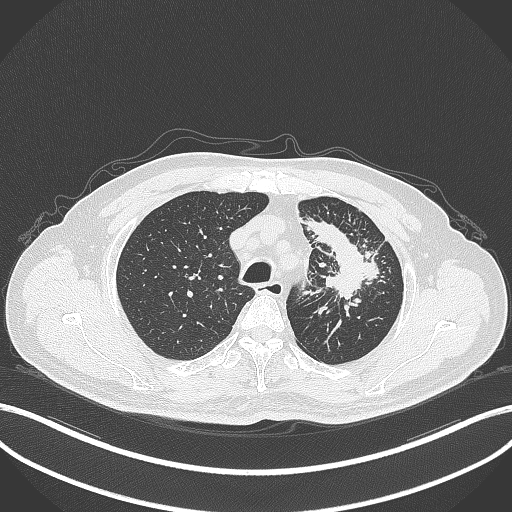
Chest CT, one axial slice; slice 279 of 386 in the series (ordered by position); reconstruction kernel B70f; 120 kVp; lung window (W 1500 / L -600 HU); 1 mm slice thickness; 512 × 512 image matrix, field of view 400 × 400 mm. Patient: male, 69 years. Case-level facts recorded for this patient, not image findings: clinical TNM (as recorded): T2a N2 M0; histopathological grade: G2-3.
Annotated regions visible in this slice (rectangle marked by the reading radiologist):
- lung tumour (recorded histology: adenocarcinoma): box from (x=304, y=216) to (x=383, y=302) px